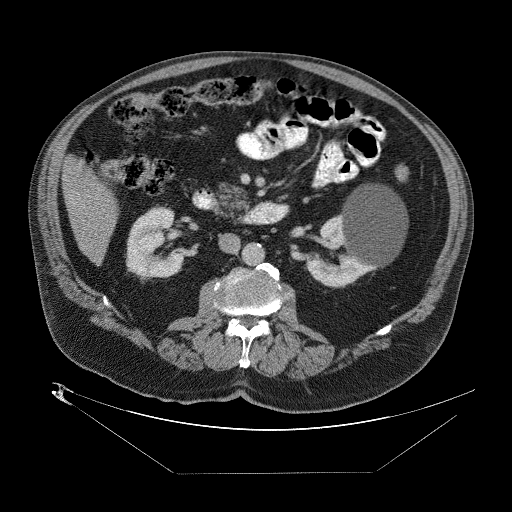
Contrast-enhanced abdominal CT (liver protocol), one axial slice. Position 14 of 89 along the scan axis. Reconstruction kernel STANDARD. 140 kVp. One of 2 acquisitions stored at this slice position. Soft-tissue window (W 400 / L 40 HU). 512 × 512 image matrix. Case-level facts recorded for this patient, not image findings: diagnosis: hepatocellular carcinoma (patient treated with transarterial chemoembolisation; whether this scan precedes or follows treatment is not stated here); TNM stage (as recorded): Stage-II; Child-Pugh class: B; tumour differentiation: moderately differentiated; tumour nodularity: multinodular.
Outlined on this slice (semi-automatic segmentation, software-assisted and operator-edited):
- abdominal aorta: bounding box [x1, y1, x2, y2] px = [244, 243, 265, 266]
- liver parenchyma outside the tumour (the mass and vessels are separate outlines, so this box may not span the whole liver): [62, 156, 118, 258]
- liver vessels: [68, 190, 79, 202]